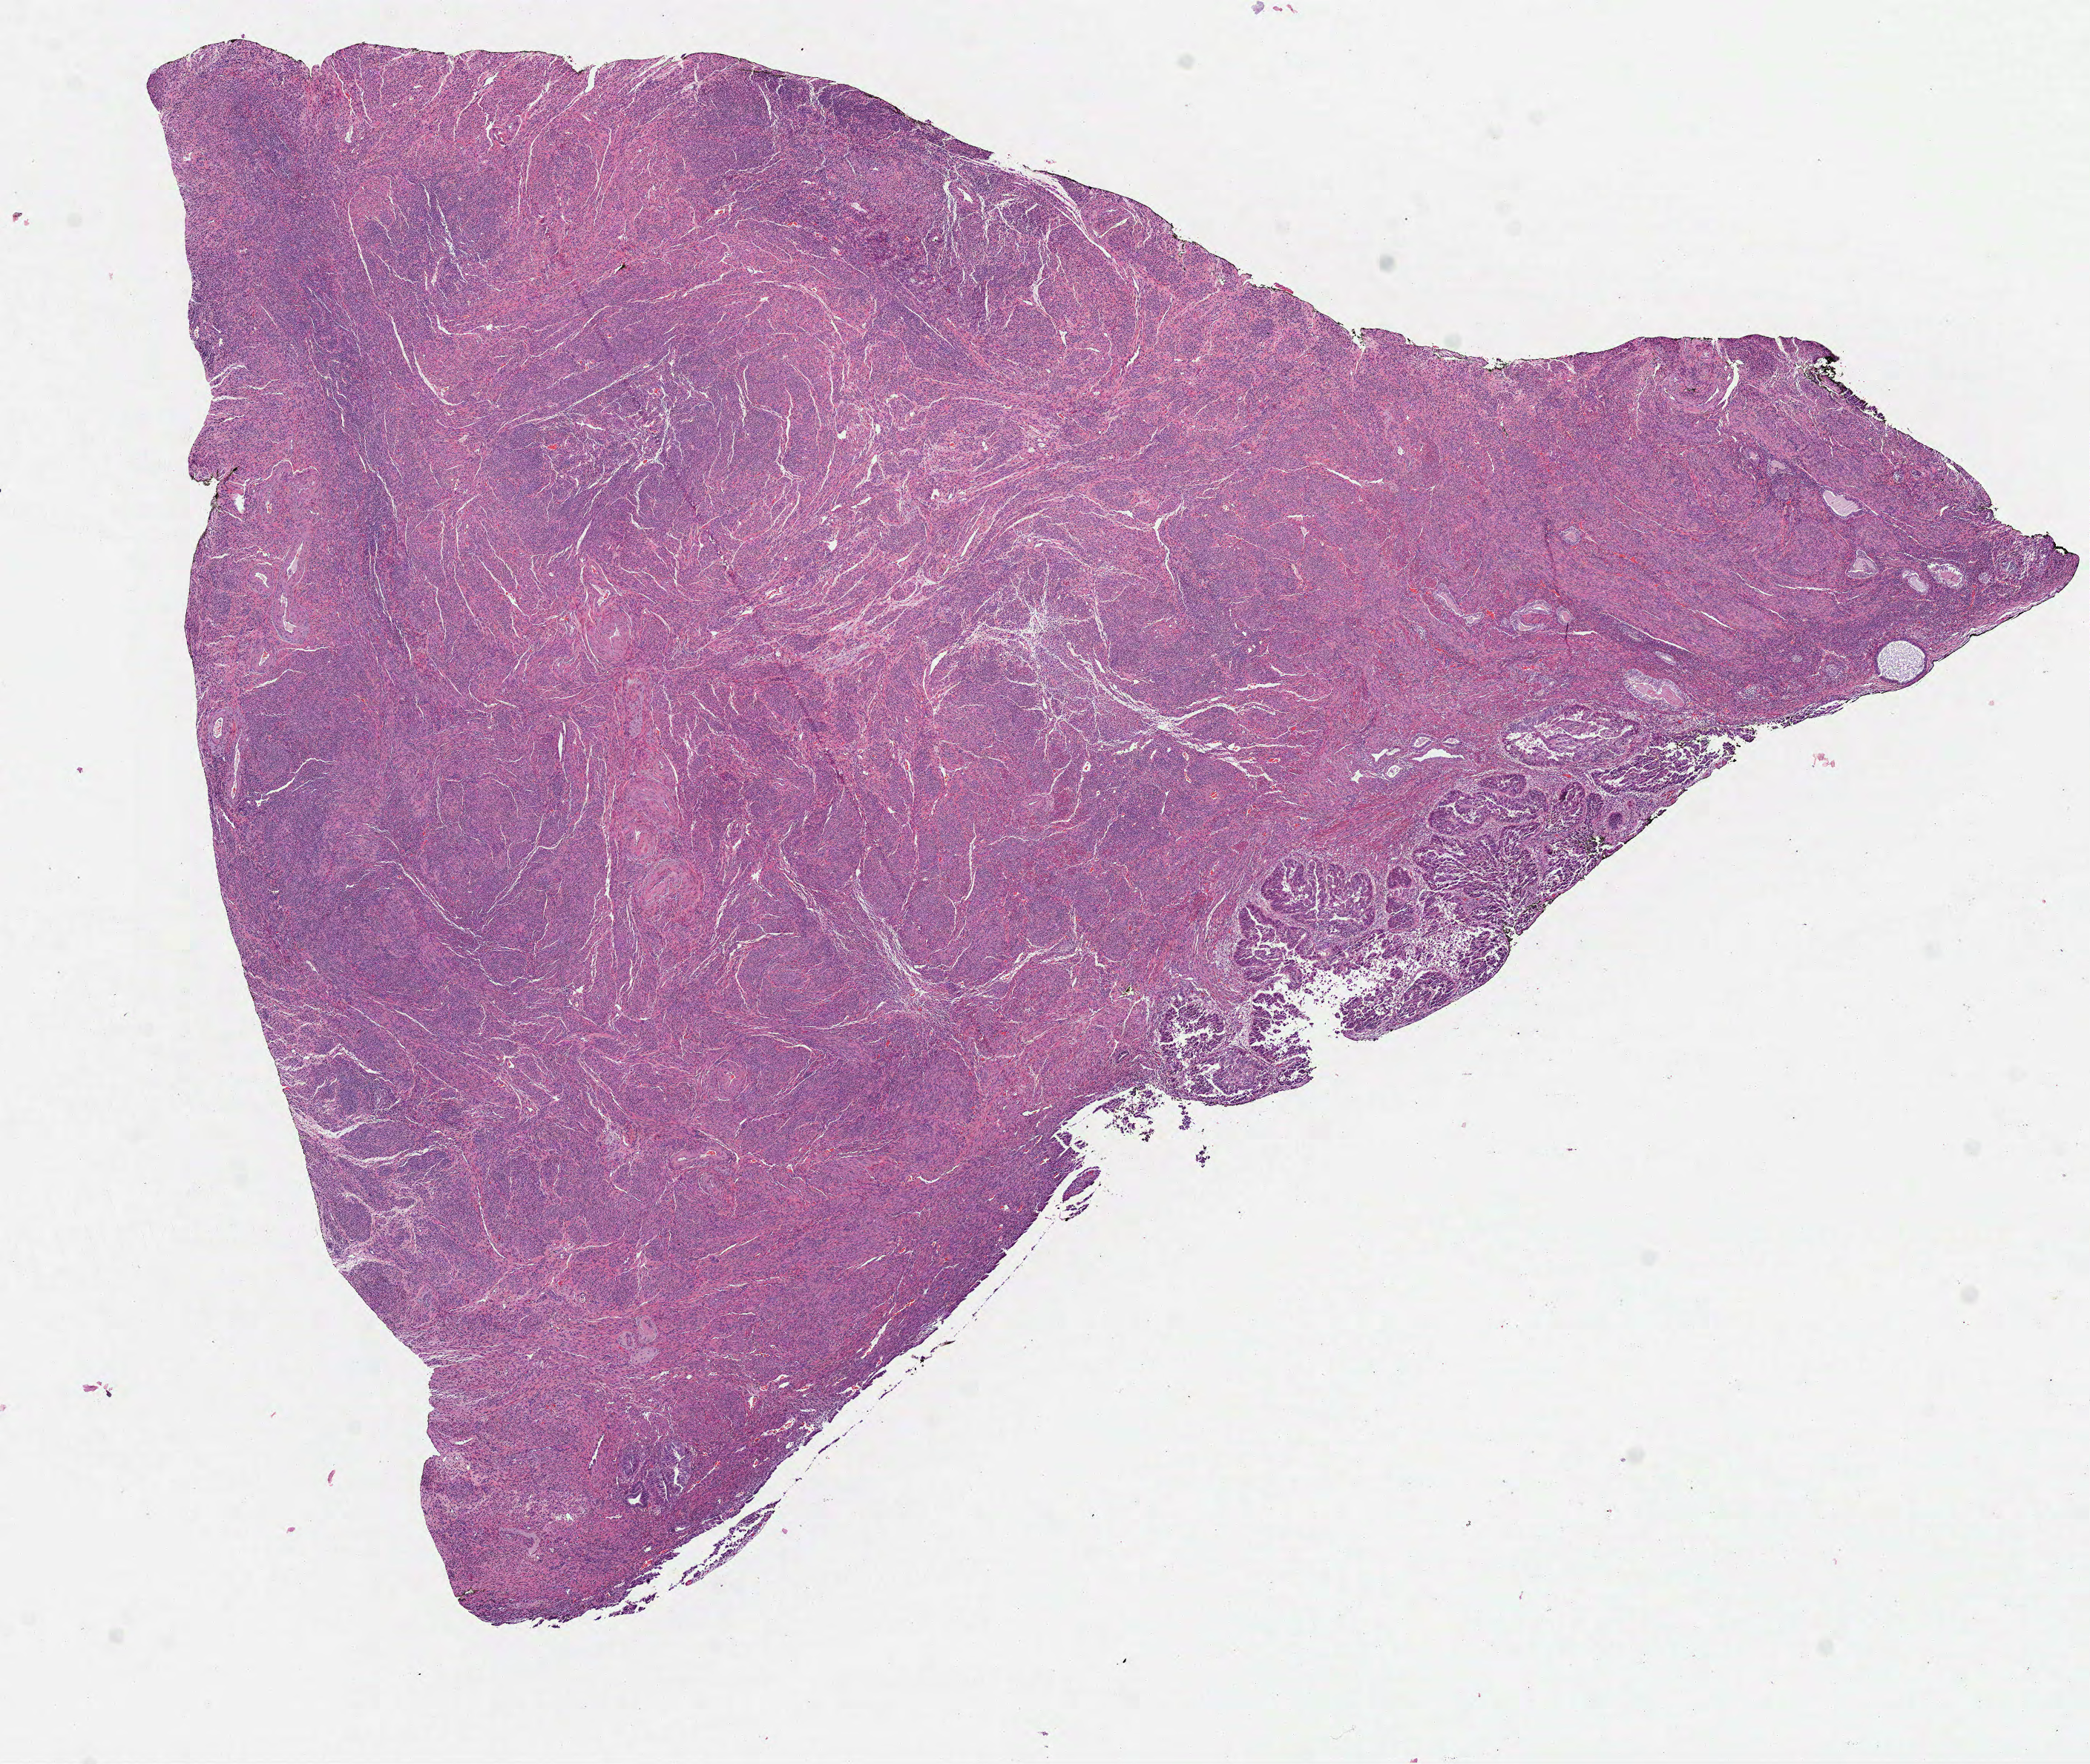
Digitized H&E-stained tissue section (whole slide), low-resolution overview of the scanned area, about 11.4 x 9.6 mm (slide scanned at 40x). Formalin-fixed paraffin-embedded (FFPE) diagnostic section. Sample: primary tumour, uterus. Patient: female, age at initial diagnosis 69 years. Histologic grade: G3 (poorly differentiated).
• FIGO stage: IB
• pathologic diagnosis: Endometrioid adenocarcinoma, NOS (endometrium)
• lymph nodes positive (case pathology): 0 of 8 examined